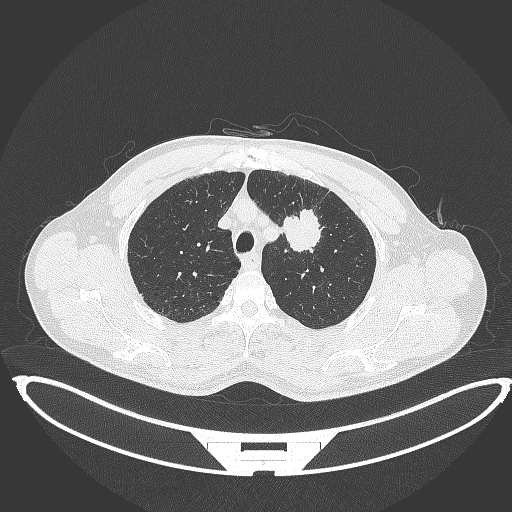
Chest CT, one axial slice; position 351 of 395 along the scan axis; 120 kVp; lung window (W 1500 / L -600 HU); 1 mm slice thickness; 512 × 512 image matrix, field of view 457 × 457 mm. Male patient, age 60 years. From the clinical record (not read from this slice): clinical TNM (as recorded): T2a N0 M0.
Structures marked on this image (rectangle marked by the reading radiologist):
- lung tumour (recorded histology: squamous cell carcinoma): bounding box [x1, y1, x2, y2] px = [281, 205, 322, 256]